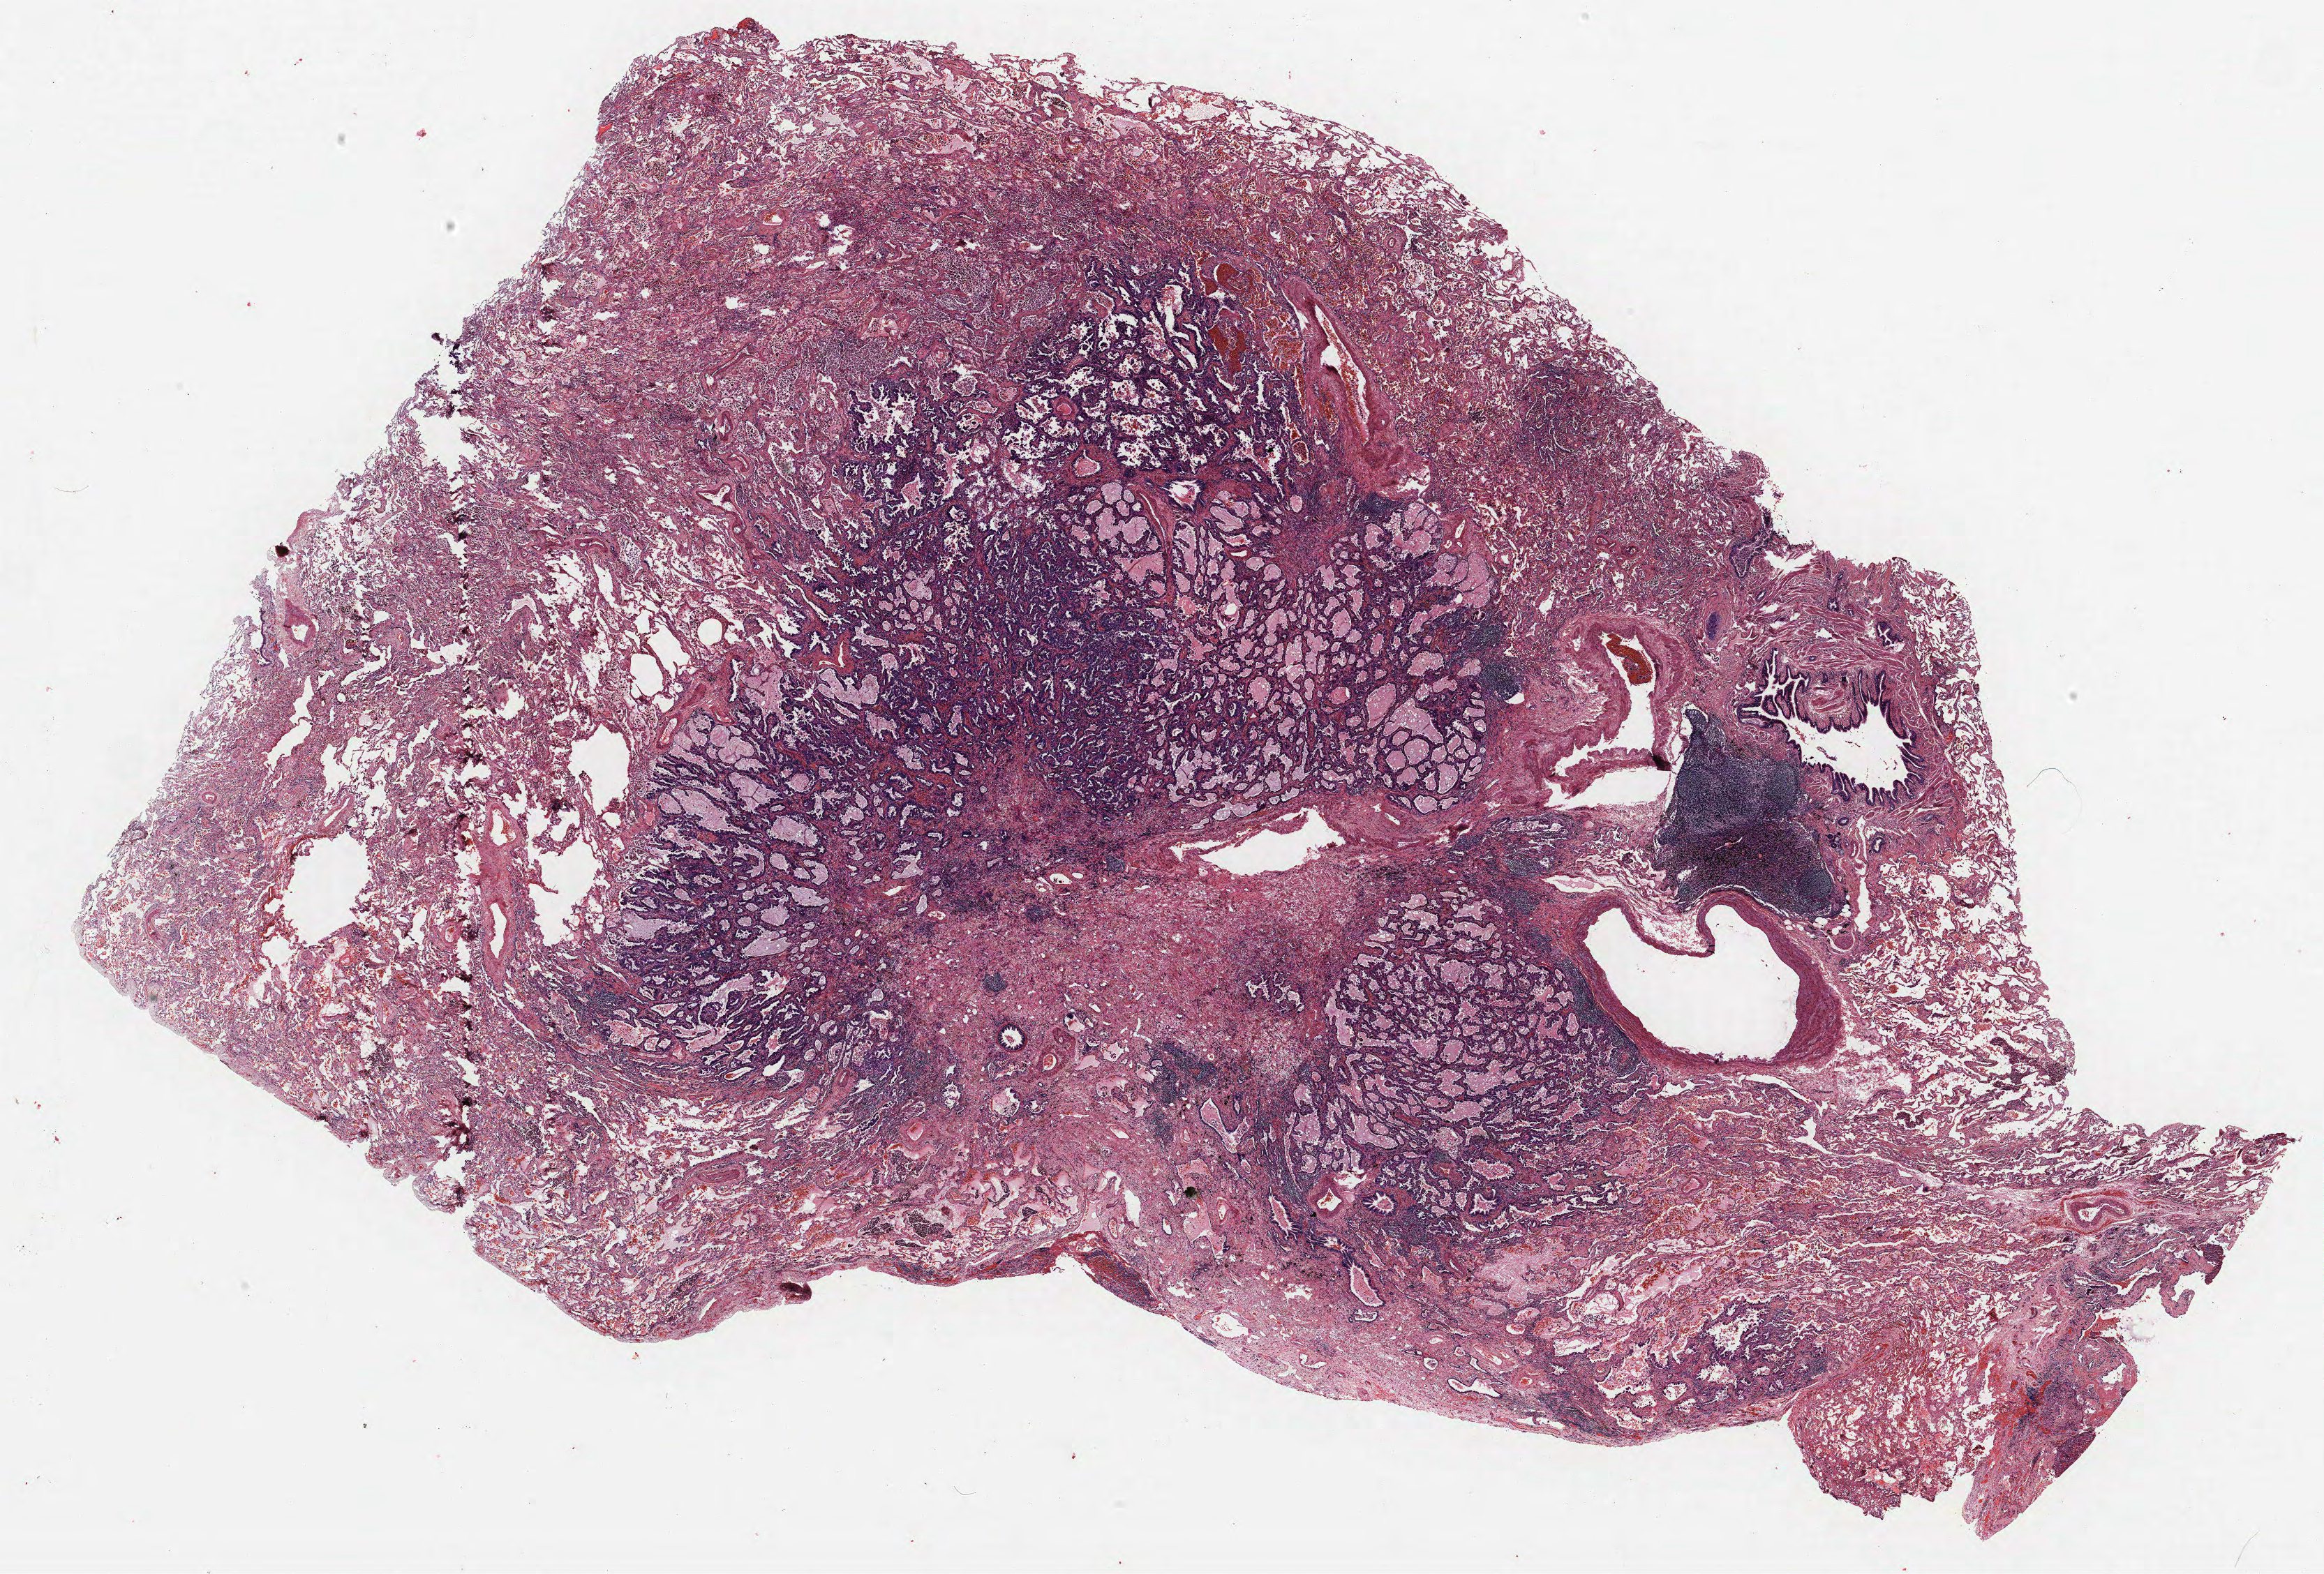
Hematoxylin and eosin (H&E) stained whole-slide image, shown as a low-resolution overview of the whole scanned area (about 26.6 x 18.1 mm, acquisition: 40x scan), formalin-fixed paraffin-embedded (FFPE) section, lung. Female, age 55 at enrolment. Current smoker at enrolment. Grade: moderately differentiated (G2).
• primary tumour location (clinical record): right lower lobe
• stage (AJCC 6th edition): IA
• tumour size (pathology): 12 mm
• ICD-O-3 topography: lower lobe of lung (C34.3)
• participant's lung-cancer diagnosis: Bronchiolo-alveolar adenocarcinoma, NOS